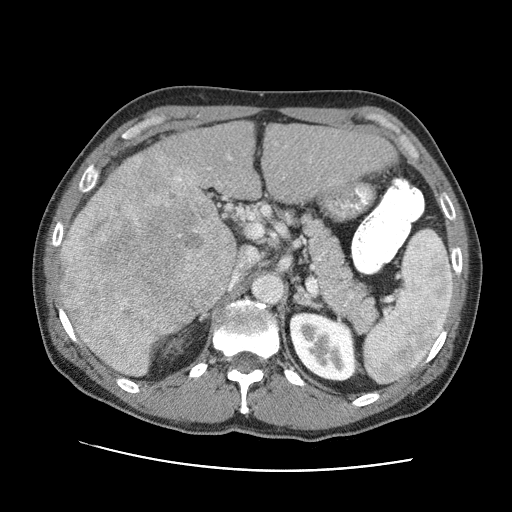
Contrast-enhanced abdominal CT (liver protocol), one axial slice; position 47 of 95 along the scan axis; reconstruction kernel STANDARD; 120 kVp; one of 2 acquisitions stored at this slice position; soft-tissue window (W 400 / L 40 HU); 2.5 mm slice thickness; 512 × 512 image matrix, field of view 360 × 360 mm. From the clinical record (not read from this slice): diagnosis: hepatocellular carcinoma (patient treated with transarterial chemoembolisation; whether this scan precedes or follows treatment is not stated here); TNM stage (as recorded): Stage-IVA; Child-Pugh class: A; tumour differentiation: moderately differentiated; tumour nodularity: multinodular.
Annotated regions visible in this slice (semi-automatic segmentation, software-assisted and operator-edited):
- liver parenchyma outside the tumour (the mass and vessels are separate outlines, so this box may not span the whole liver): bounding box (x1, y1, x2, y2) in pixels: (60, 122, 394, 367)
- mass: (59, 154, 237, 377)
- liver vessels: (136, 155, 232, 183)